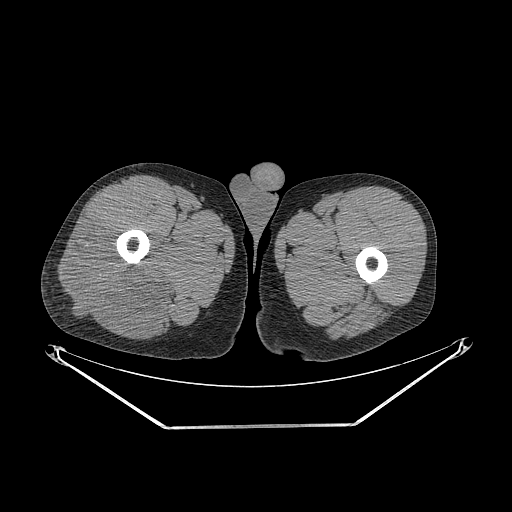
CT of an extremity soft-tissue mass (from a PET/CT study), one axial slice; slice 262 of 267 in the series (ordered by position); 140 kVp; soft-tissue window (W 400 / L 40 HU); 3.75 mm slice thickness; 512 × 512 image matrix, field of view 500 × 500 mm. Male patient. From the clinical record (not read from this slice): histological type: poorly differentiated synovial sarcoma; grade: high; site of the primary tumour: right buttock.
Annotated regions visible in this slice (expert contour drawn on MRI and transferred to this co-registered scan by the dataset authors):
- gross tumour volume including surrounding oedema: bounding box [x1, y1, x2, y2] px = [55, 222, 177, 334]
- gross tumour volume (mass): [55, 222, 163, 334]